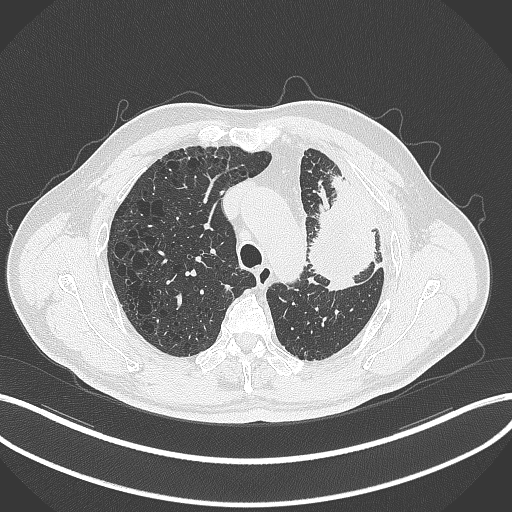
Chest CT, one axial slice; slice 234 of 297 in the series (ordered by position); reconstruction kernel B70f; lung window (W 1500 / L -600 HU); 1 mm slice thickness; 512 × 512 image matrix, field of view 400 × 400 mm. Male patient, age 68 years. Case-level facts recorded for this patient, not image findings: clinical TNM (as recorded): T3 N3 M1.
Annotated regions visible in this slice (bounding box drawn by a radiologist):
- lung tumour (recorded histology: adenocarcinoma): box from (x=303, y=166) to (x=381, y=295) px